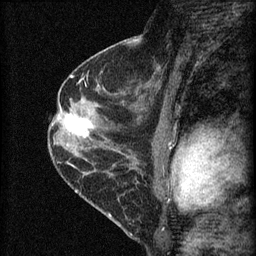
Breast MRI (dynamic contrast-enhanced), one sagittal slice. Position 37 of 60 along the scan axis. Dynamic contrast-enhanced series, image 2 of 4 at this slice position (ordered by acquisition). 1.5 T. TE 4.2 ms, TR 8.2 ms. 2 mm slice thickness. 256 × 256 image matrix, field of view 180 × 180 mm. Female patient, age 45 years.
Annotated regions visible in this slice (semi-automatically segmented with operator editing):
- analysis volume of interest (the breast-tissue region the enhancement analysis was run in; not a lesion): bounding box <58,107,98,147> (left, top, right, bottom; pixels)
- tumour enhancement mask (voxels above the 70 % enhancement threshold inside the analysis volume of interest): <65,114,93,137>